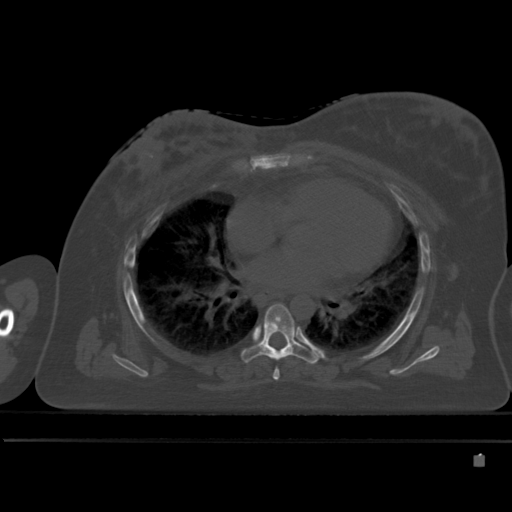
CT including the spine, one axial slice. Slice 308 of 495 in the series (ordered by position). Bone window (W 1800 / L 400 HU). 1.5 mm slice thickness. 512 × 512 image matrix. Female patient, age 33 years. Case-level facts recorded for this patient, not image findings: primary cancer: breast; vertebrae with lytic lesions (as recorded): T1.
Annotated regions visible in this slice (semi-automatic segmentation, software-assisted and operator-edited):
- T5 vertebra: bounding box (x1, y1, x2, y2) in pixels: (273, 369, 280, 380)
- T6 vertebra: (241, 304, 322, 364)